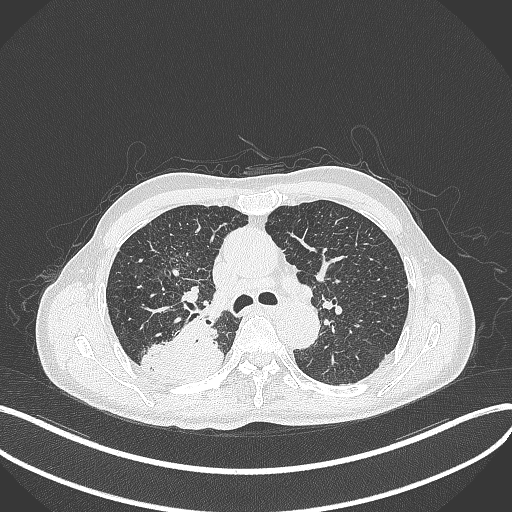
Chest CT, one axial slice; reconstruction kernel B70f; 120 kVp; lung window (W 1500 / L -600 HU); 512 × 512 image matrix, field of view 400 × 400 mm. Male patient, age 79 years. From the clinical record (not read from this slice): clinical TNM (as recorded): T3 N0 M0.
Structures marked on this image (rectangle marked by the reading radiologist):
- lung tumour (recorded histology: adenocarcinoma): bounding box (x1, y1, x2, y2) in pixels: (137, 317, 227, 382)